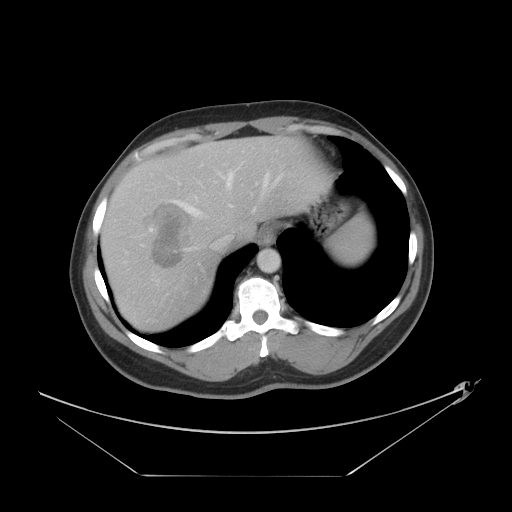
Contrast-enhanced abdominal CT, one axial slice; slice 34 of 44 in the series (ordered by position); reconstruction kernel STANDARD; 120 kVp; intravenous contrast given; soft-tissue window (W 400 / L 40 HU); 512 × 512 image matrix. Male patient, age 49 years. From the clinical record (not read from this slice): diagnosis: colorectal cancer liver metastases, imaged before liver resection; multiple liver metastases: no; largest metastasis: 8.5 cm; chemotherapy before resection: yes.
Annotated regions visible in this slice (expert manual segmentation):
- hepatic veins: bounding box (x1, y1, x2, y2) in pixels: (170, 170, 284, 251)
- liver: (101, 136, 332, 333)
- planned liver remnant (the part of the liver to remain after resection): (194, 136, 332, 246)
- portal vein (with intrahepatic branches): (150, 228, 153, 232)
- liver metastasis: (146, 203, 192, 269)